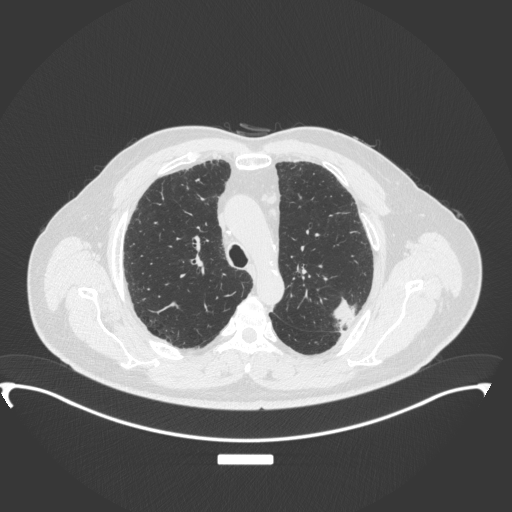
Chest CT, one axial slice. Slice 259 of 350 in the series (ordered by position). Lung window (W 1500 / L -600 HU). 1 mm slice thickness. 512 × 512 image matrix, field of view 459 × 459 mm. Male patient, age 64 years. From the clinical record (not read from this slice): clinical TNM (as recorded): T1c N1 M1.
Annotated regions visible in this slice (rectangle marked by the reading radiologist):
- lung tumour (recorded histology: adenocarcinoma): box from (x=326, y=292) to (x=363, y=331) px